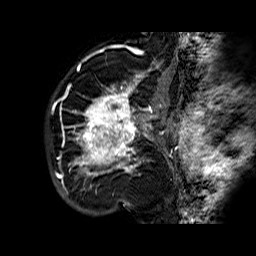
Breast MRI (dynamic contrast-enhanced), one sagittal slice. Slice 47 of 60 in the series (ordered by position). Dynamic contrast-enhanced series, time point 2 of 6 at this slice position (early post-contrast). 1.5 T. TE 6.3 ms, TR 32.4 ms. 4 mm slice thickness. 256 × 256 image matrix, field of view 200 × 200 mm. Female patient. Case-level facts recorded for this patient, not image findings: setting: breast cancer imaged before/during neoadjuvant chemotherapy; receptor status: HR-positive, HER2-negative.
Annotated regions visible in this slice (semi-automatic segmentation, software-assisted and operator-edited):
- analysis volume of interest (the breast-tissue region the enhancement analysis was run in; not a lesion): box from (x=68, y=72) to (x=177, y=183) px
- tumour enhancement mask (voxels above the 100 % enhancement threshold inside the analysis volume of interest): (x=72, y=74)–(x=177, y=176)